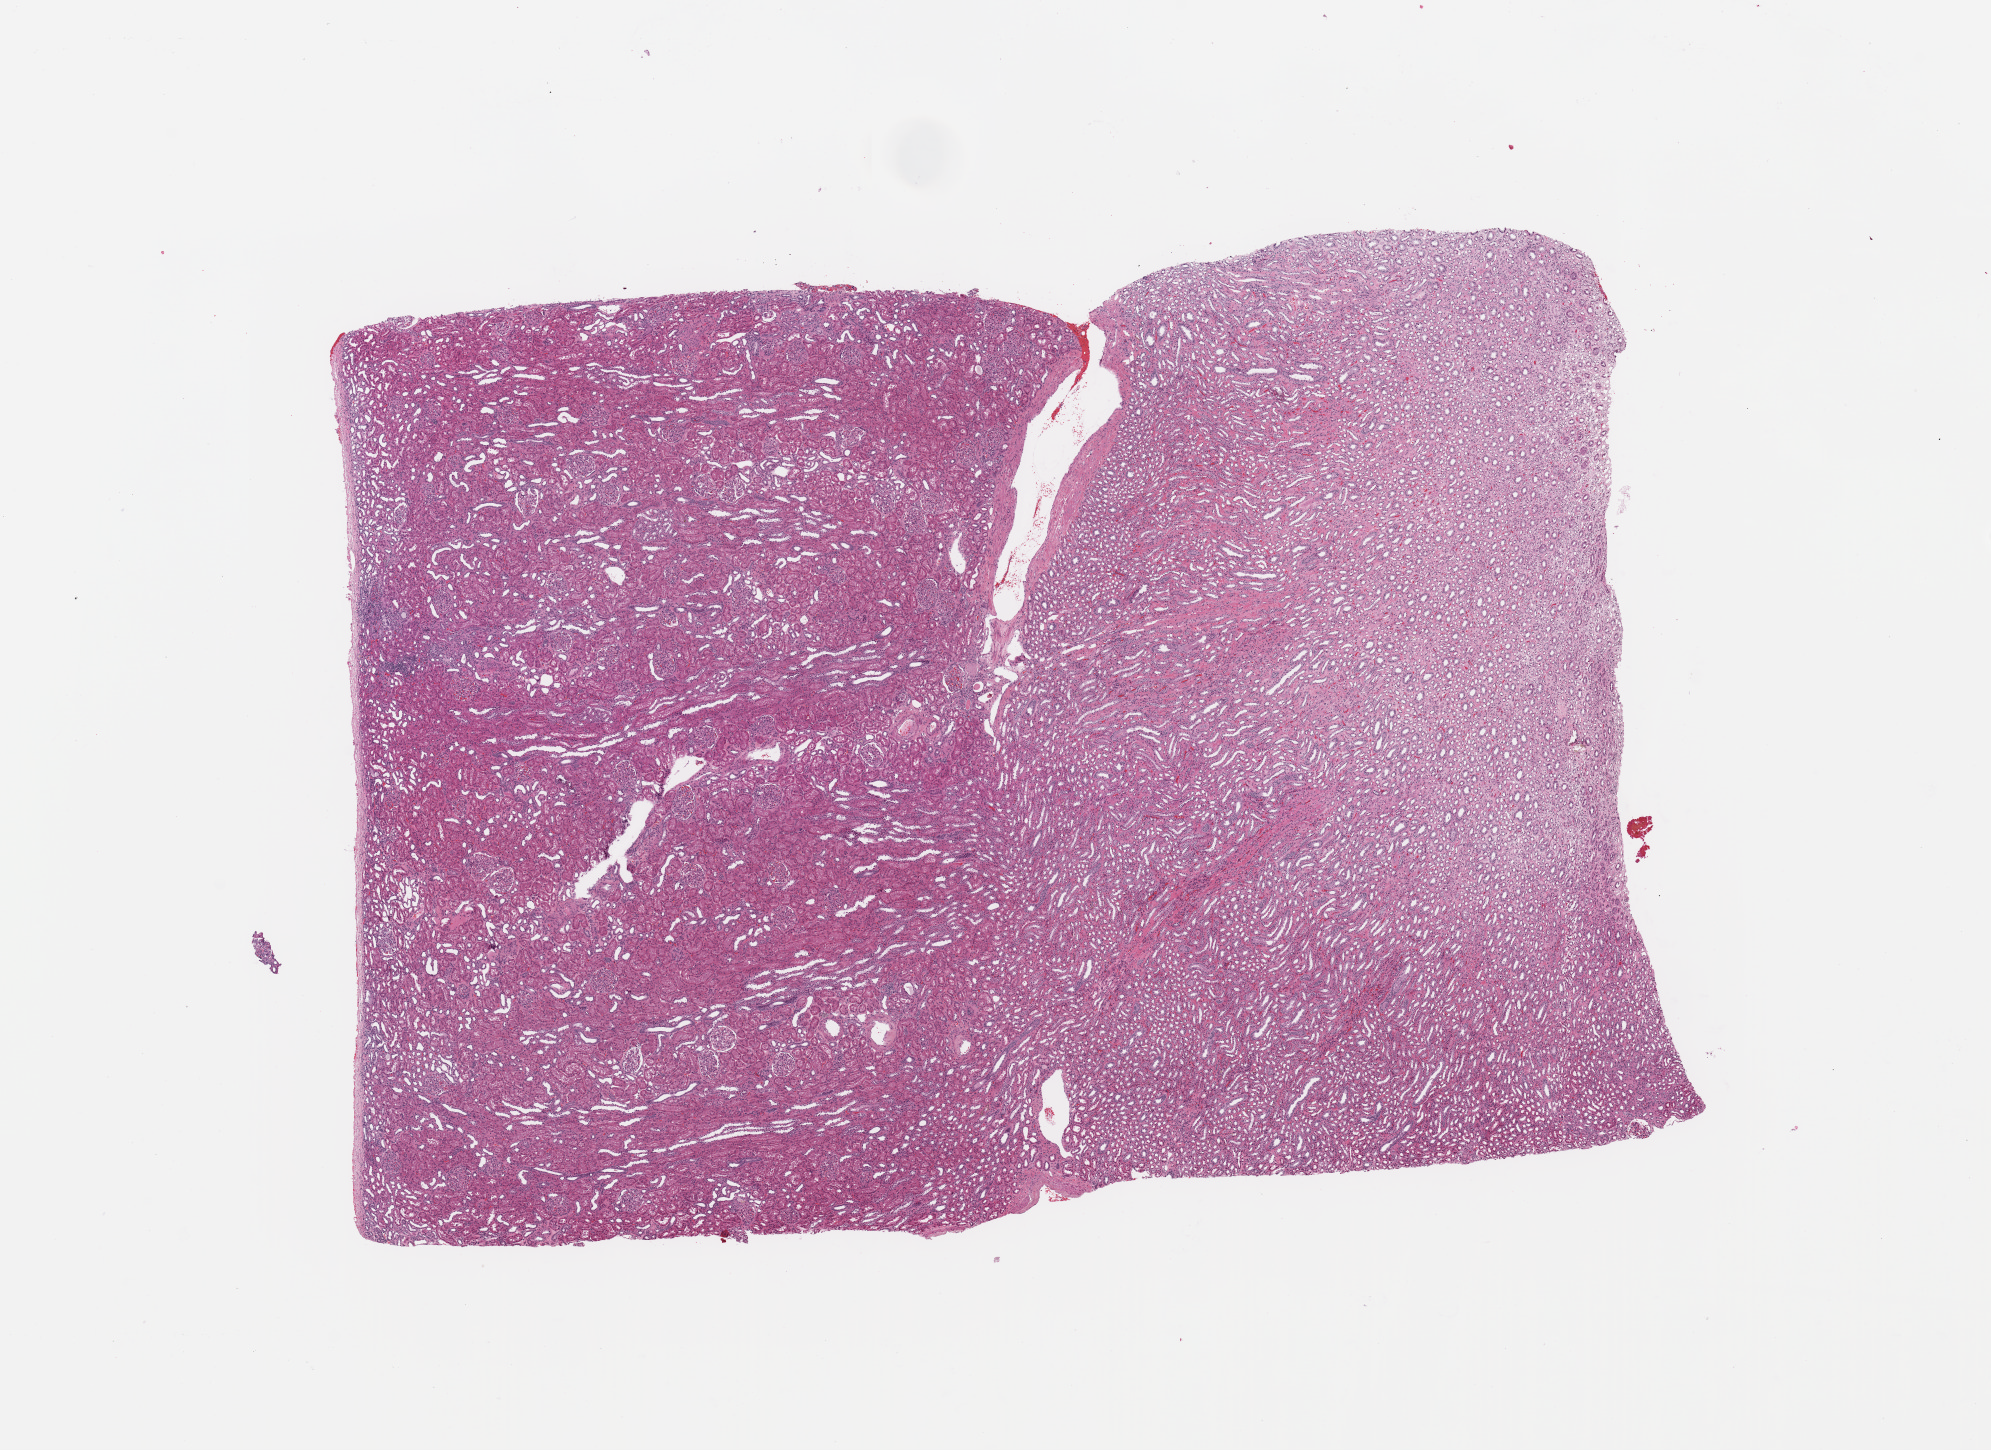
H&E whole-slide image — low-resolution overview of the scanned area, about 15.8 x 11.5 mm (slide scanned at 20x). Normal (non-tumour) tissue sample, sampled site: kidney. Male, 55 y/o.
This section: normal (non-tumour) tissue from the same patient. Patient diagnosis: Renal cell carcinoma, NOS.